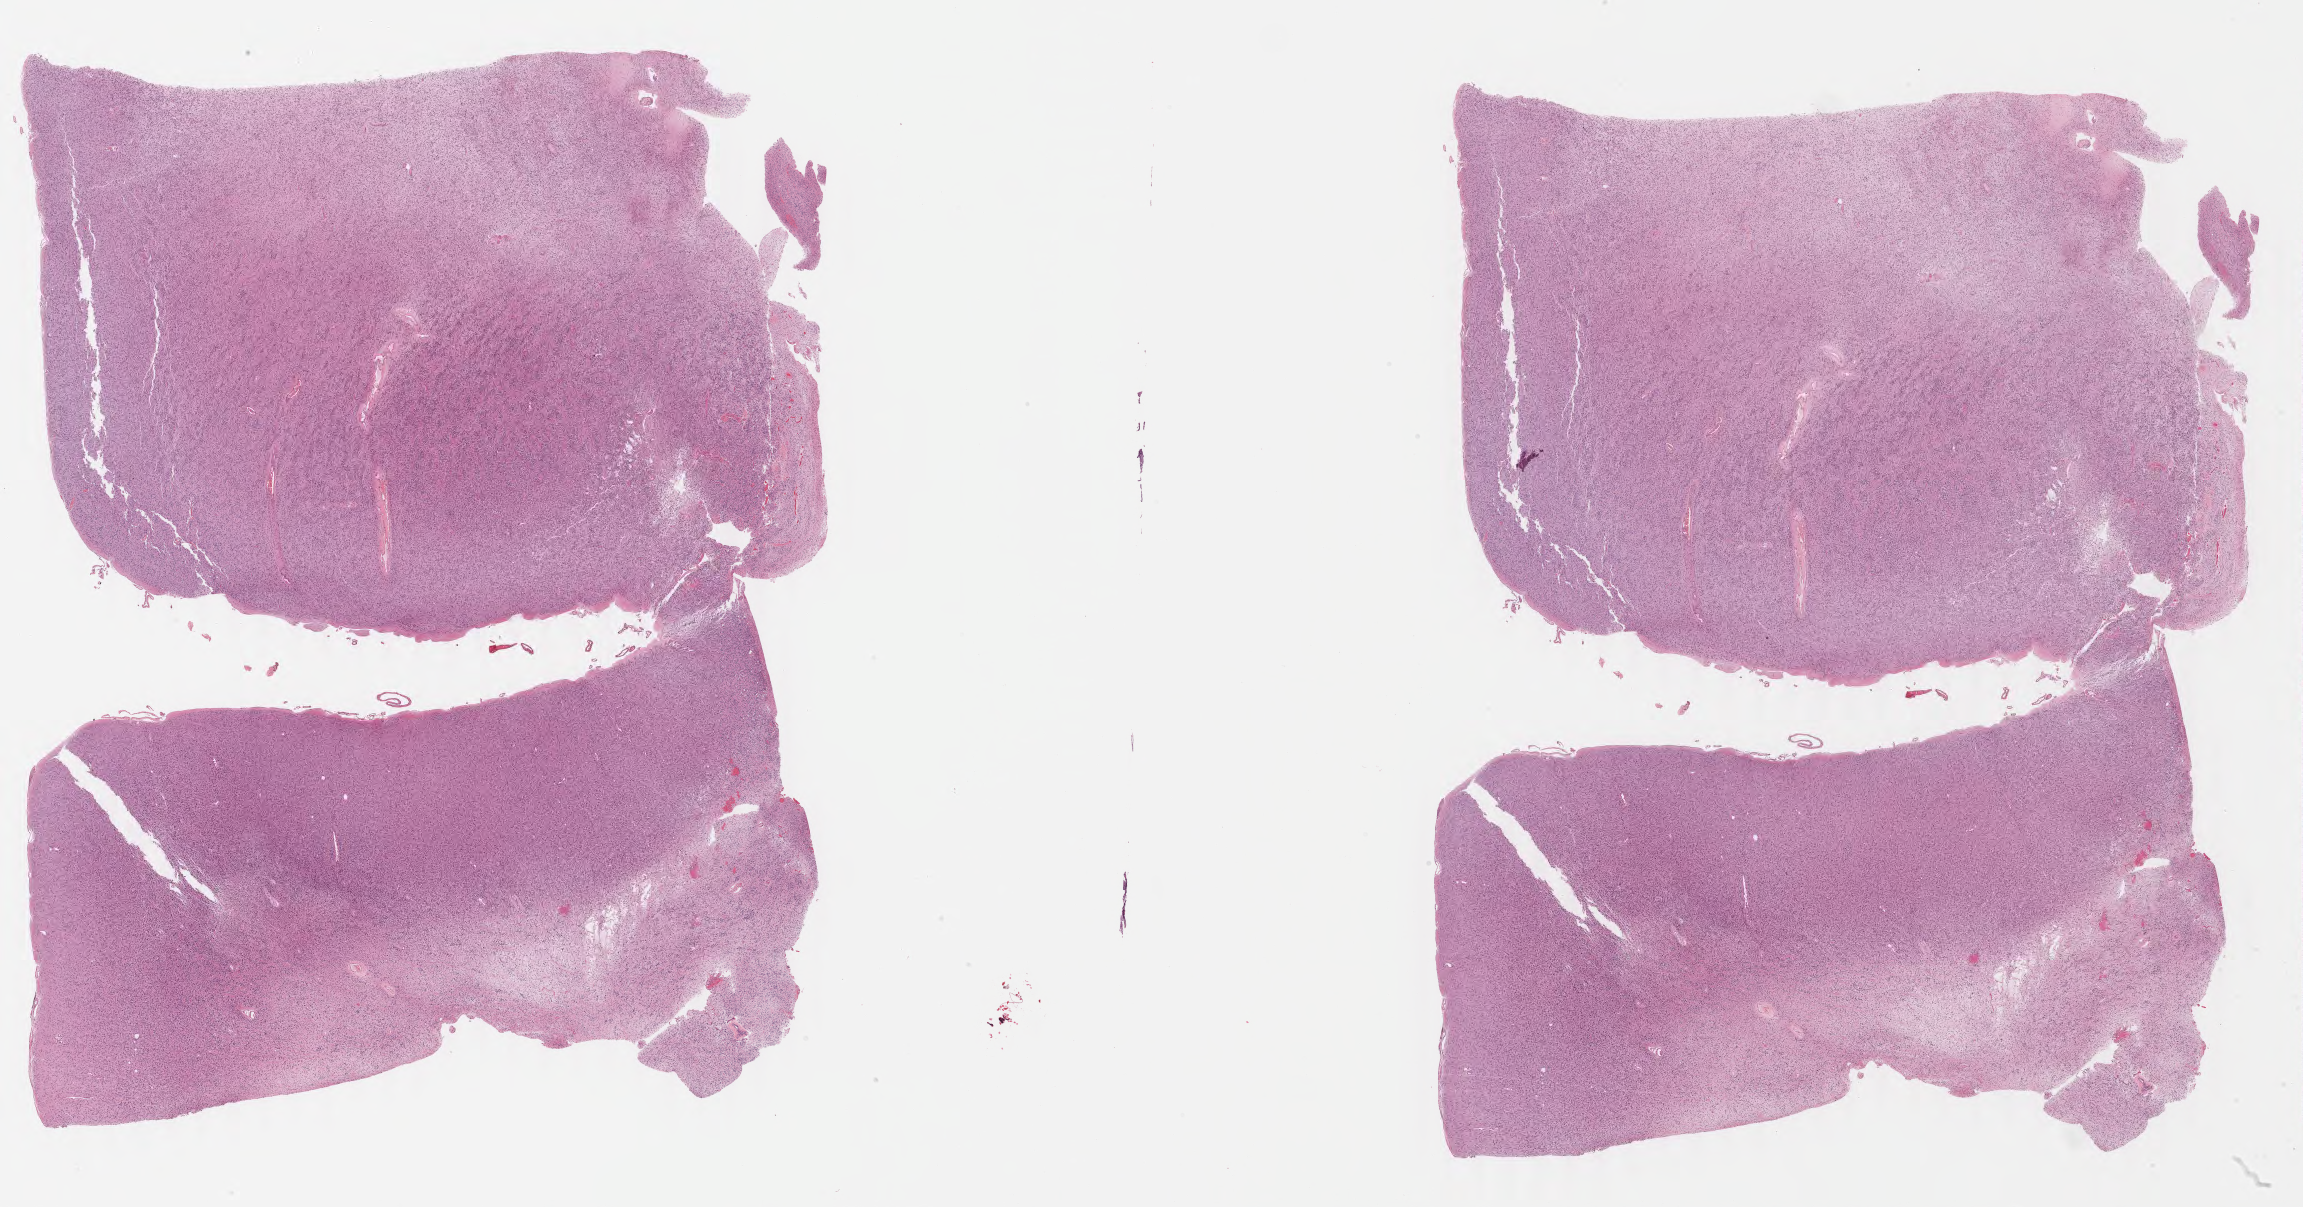
Whole-slide histology image, H&E — shown as a low-resolution overview of the whole scanned area (about 36.4 x 19.1 mm), FFPE section, brain, primary tumour sample. Female patient; age at initial diagnosis 56 years. Histologic grade: G3 (poorly differentiated).
* pathologic diagnosis: Astrocytoma, anaplastic (cerebrum)